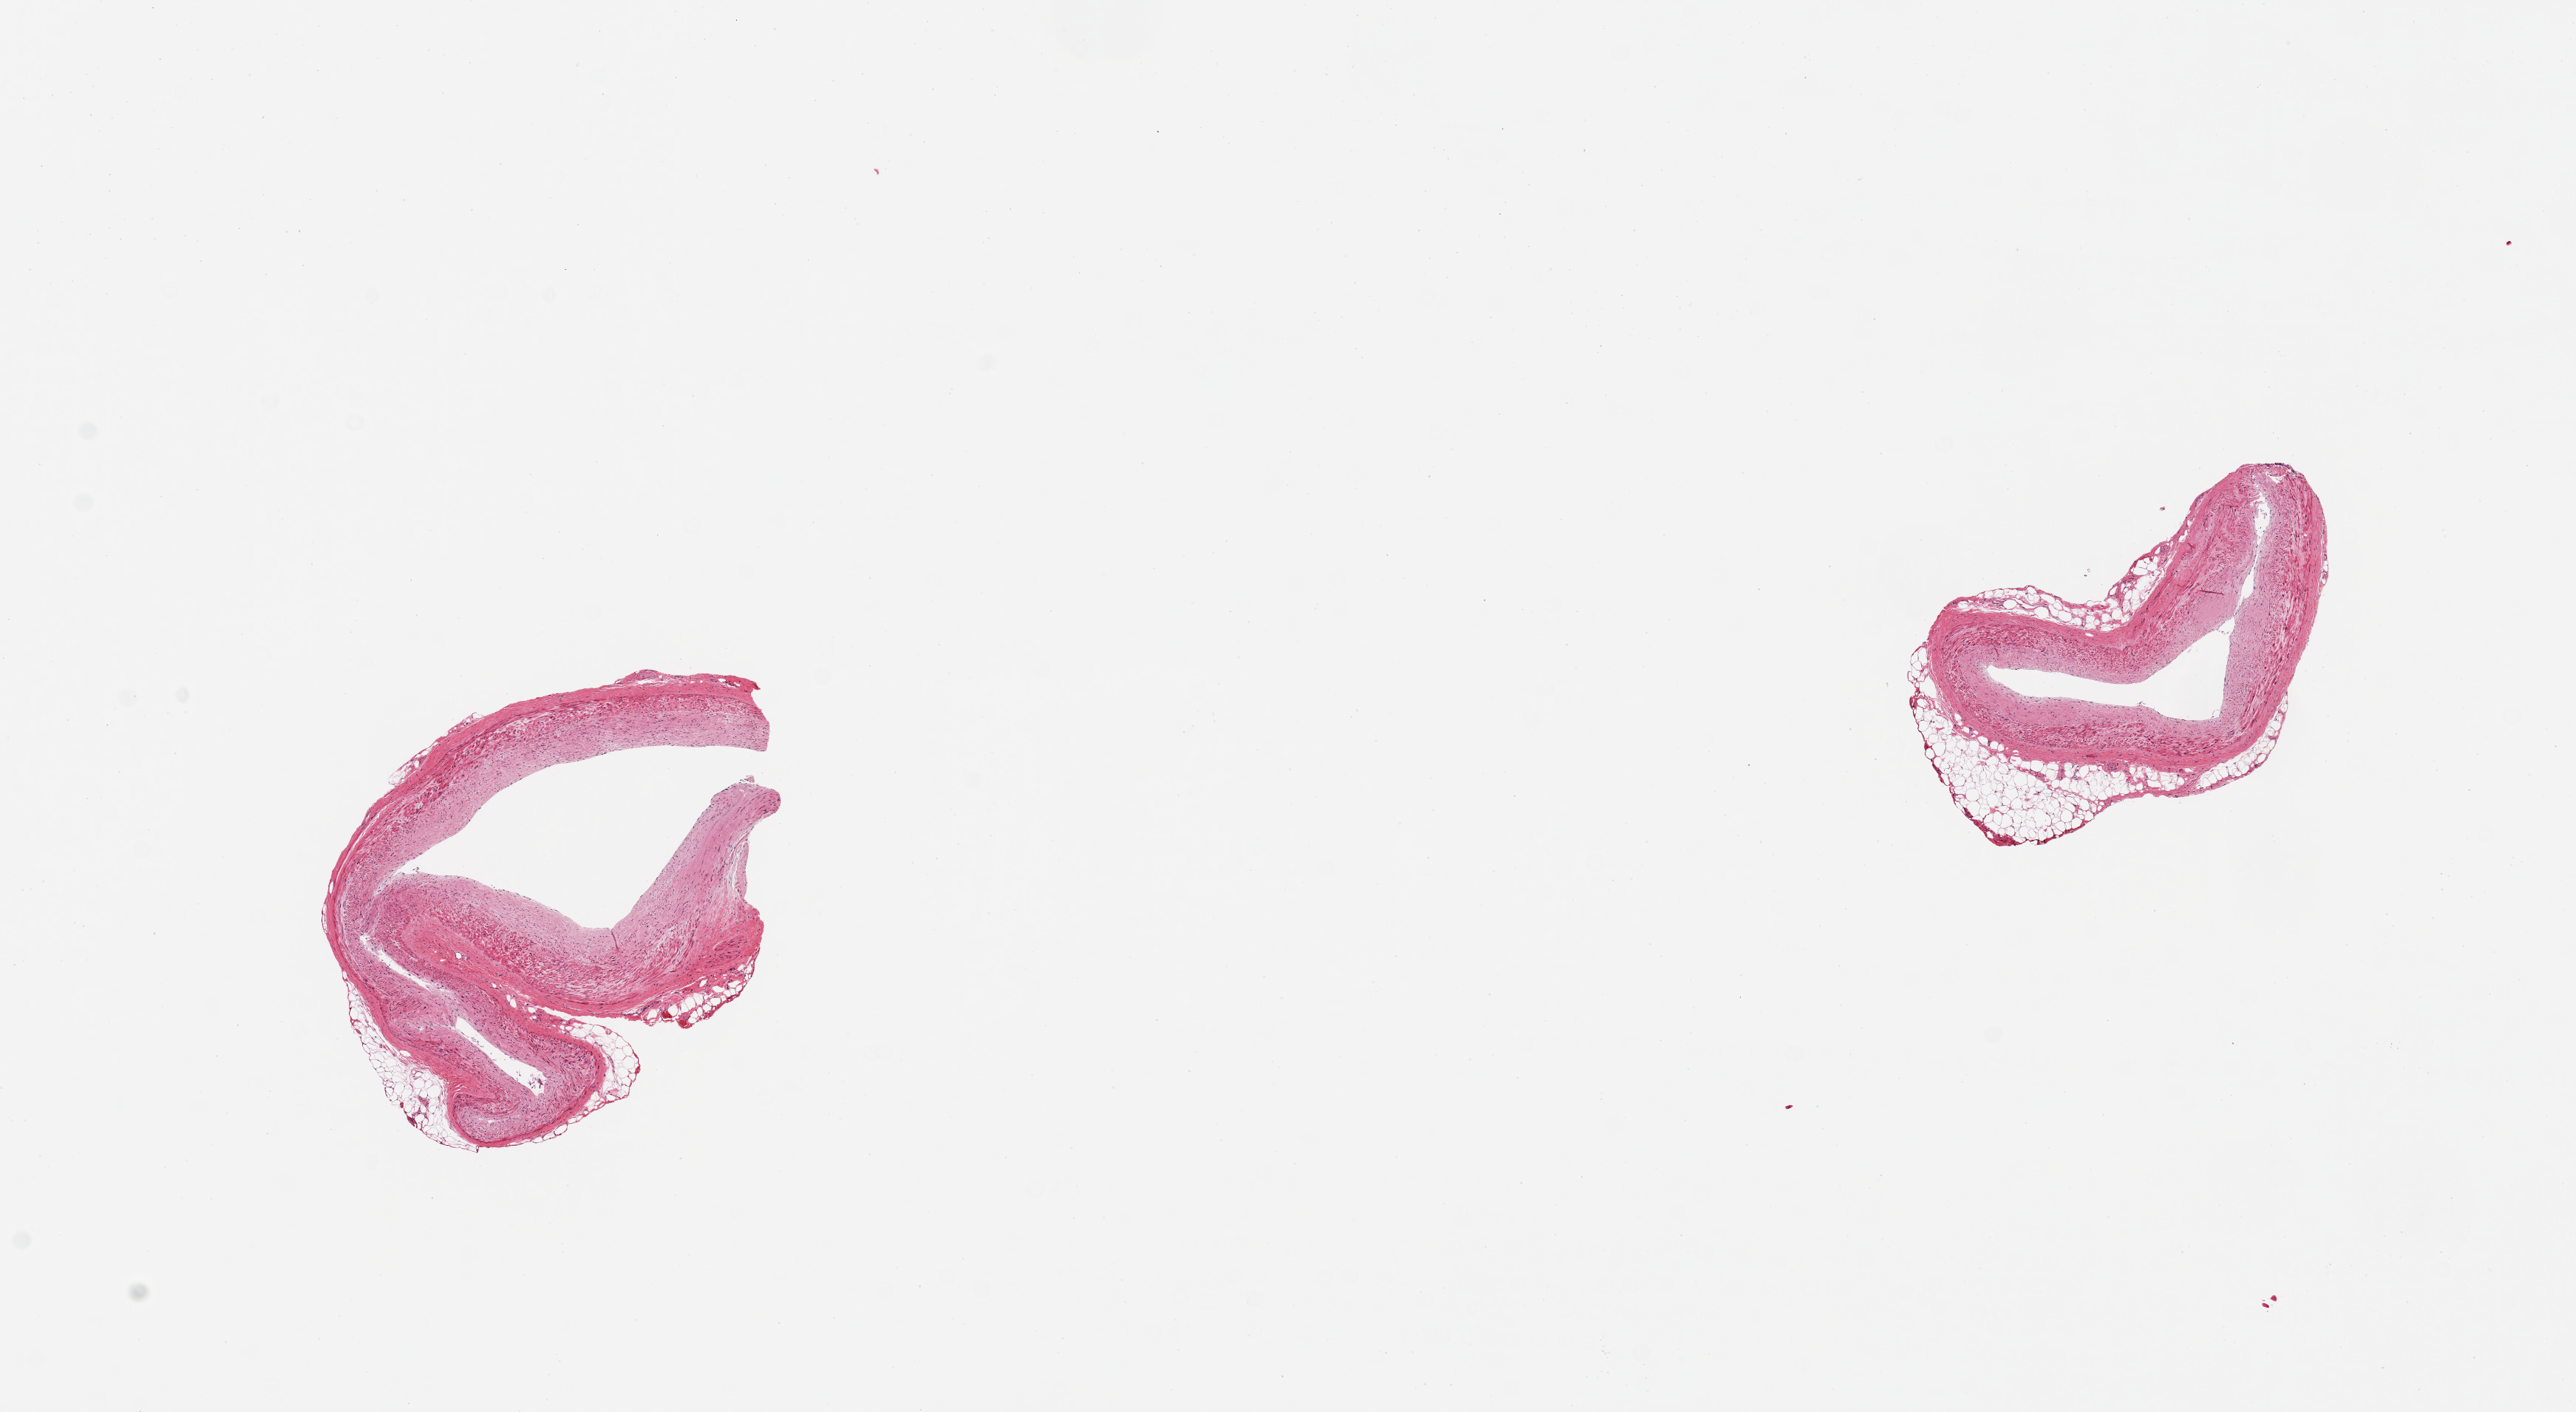
H&E whole-slide image — whole scanned area (about 13.8 x 7.6 mm) shown as a low-resolution overview; PAXgene-fixed paraffin-embedded (PFPE) section; target tissue: coronary artery; tissue donor sample. Donor: male.
Reviewer comment on this tissue sample: 2 pieces; mild plaque, patent lumen; 20% external fat.